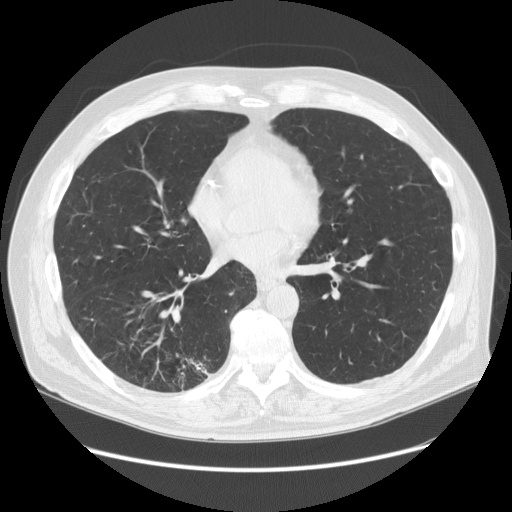
Low-dose screening chest CT, one axial slice. Slice 64 of 149 in the series (ordered by position). Reconstruction kernel STANDARD. Lung window (W 1500 / L -600 HU). 2.5 mm slice thickness. 512 × 512 image matrix, field of view 400 × 400 mm.
Structures marked on this image (expert manual segmentation):
- lesion 1 (tumor, lower lobe of right lung): box from (x=178, y=358) to (x=206, y=375) px